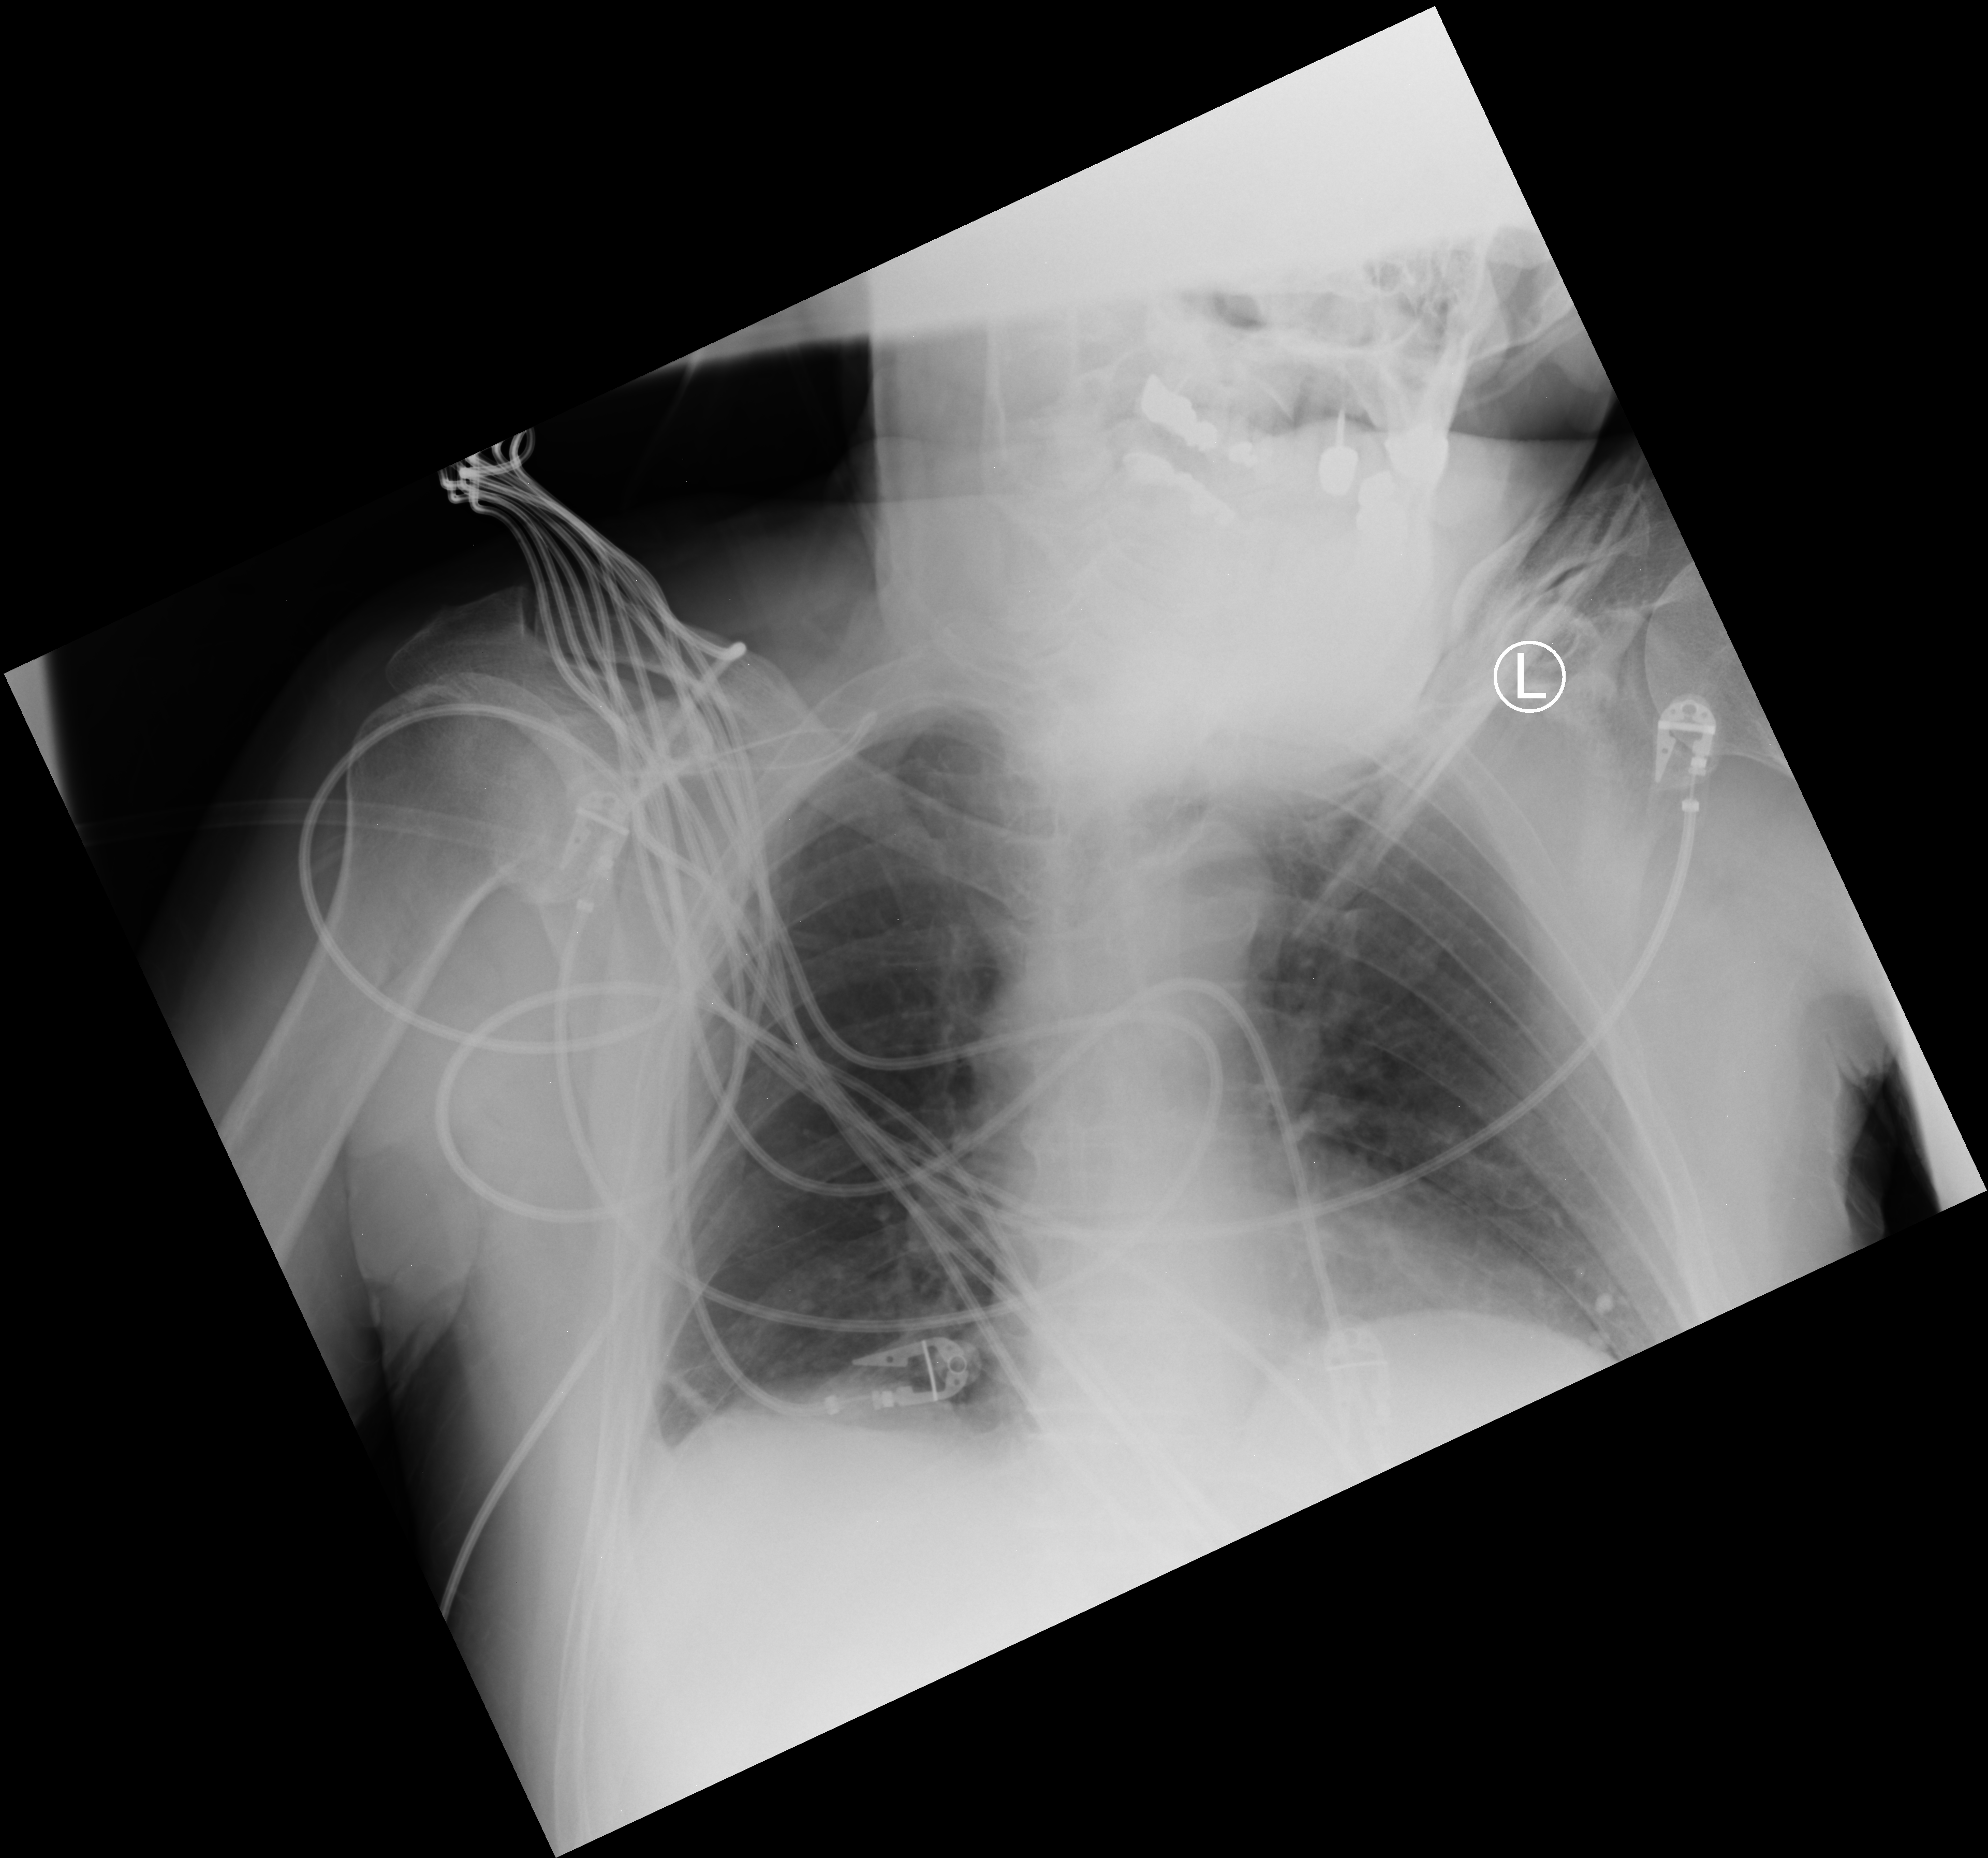
Chest X-ray (portable), anteroposterior (AP) projection. Patient hospitalised with COVID-19; male, aged 75–90 years.
Admission-level facts for this patient (not findings on this image; timing relative to this image not recorded): admitted to intensive care during this hospital stay: no.